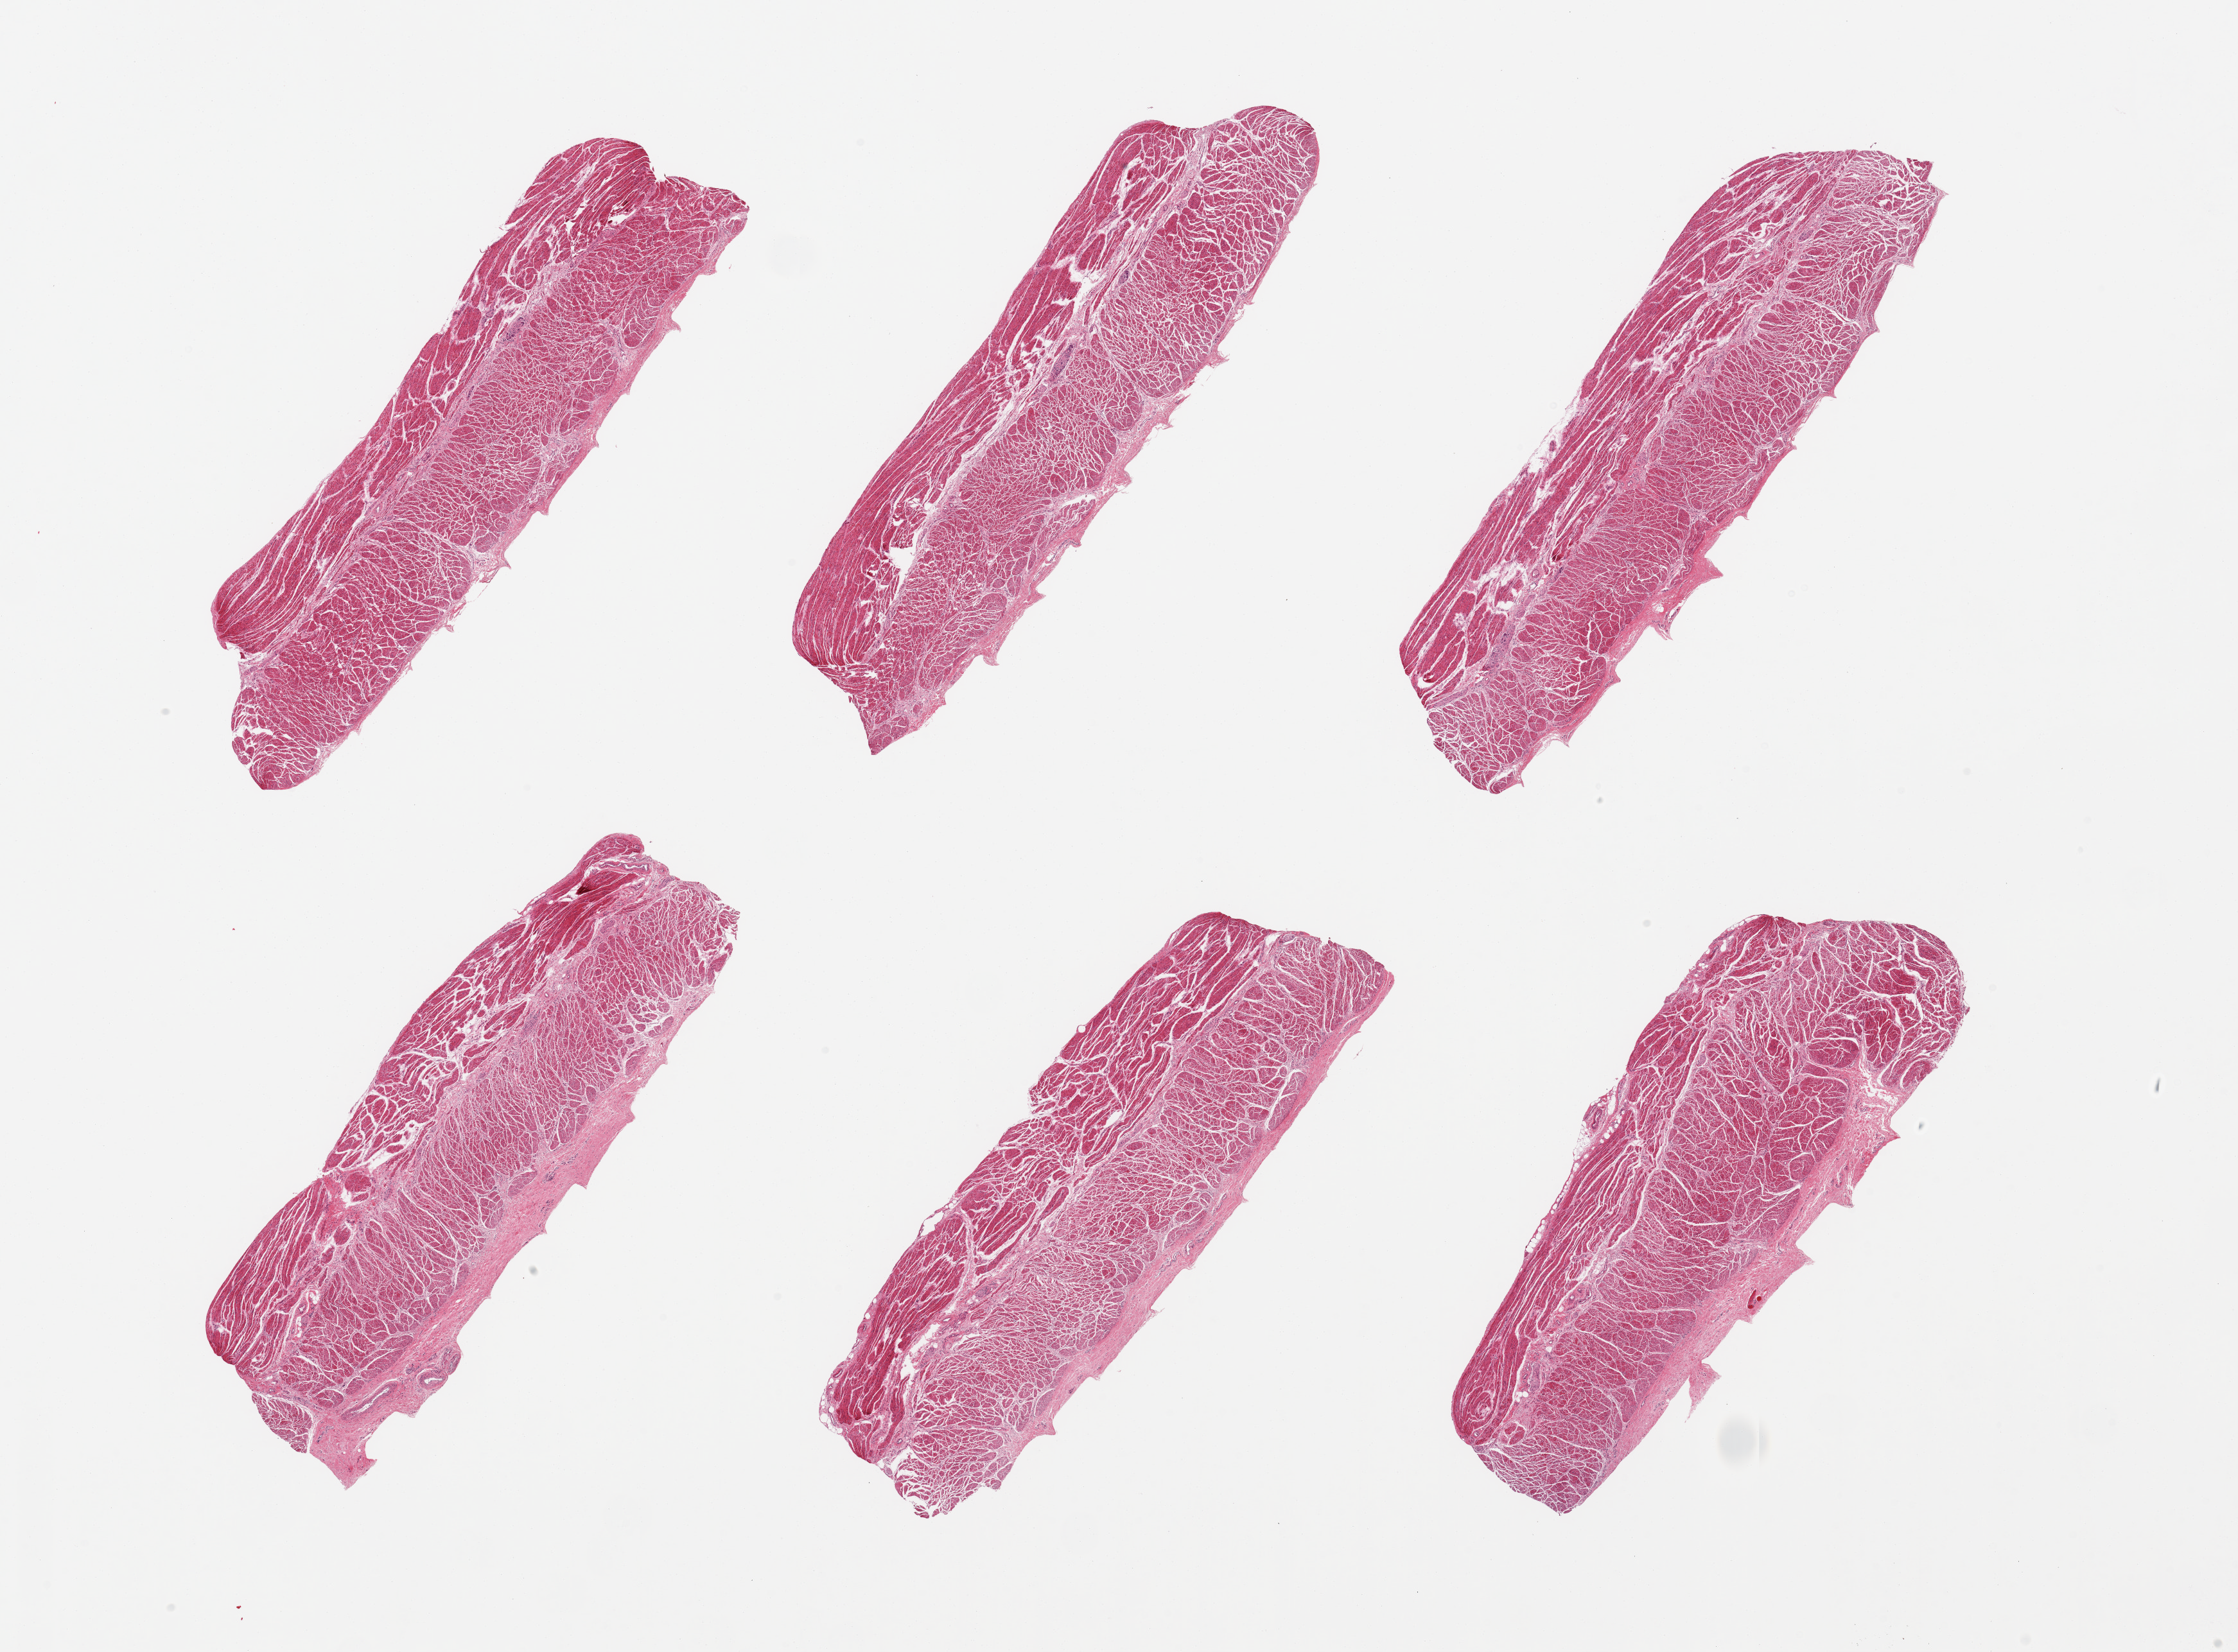
H&E whole-slide image, brightfield, a low-resolution overview of the entire scanned area, about 27.6 x 20.4 mm; PAXgene-fixed paraffin-embedded (PFPE) section; target tissue: esophageal muscle; donor tissue sample. Male donor.
Reviewer comment on this tissue sample: 6 pieces, all target muscularis.